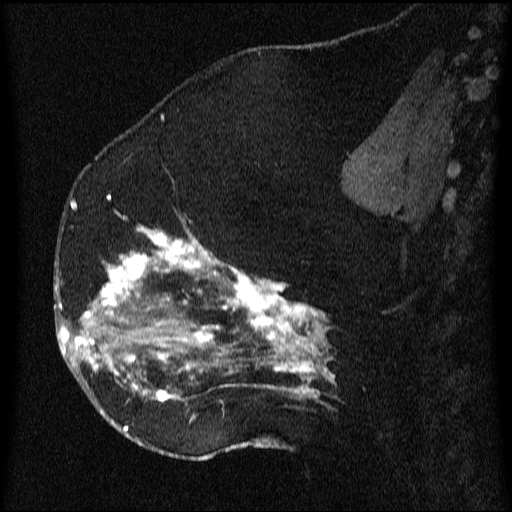
Breast MRI (dynamic contrast-enhanced), one sagittal slice. Position 36 of 64 along the scan axis. Dynamic contrast-enhanced series, image 2 of 3 at this slice position (ordered by acquisition). 1.5 T. TE 4.2 ms, TR 9.1 ms. 2.2 mm slice thickness. 512 × 512 image matrix. Female patient, age 52 years.
Structures marked on this image (semi-automatic segmentation, software-assisted and operator-edited):
- analysis volume of interest (the breast-tissue region the enhancement analysis was run in; not a lesion): box from (x=61, y=203) to (x=336, y=438) px
- tumour enhancement mask (voxels above the 70 % enhancement threshold inside the analysis volume of interest): (x=61, y=203)–(x=336, y=433)